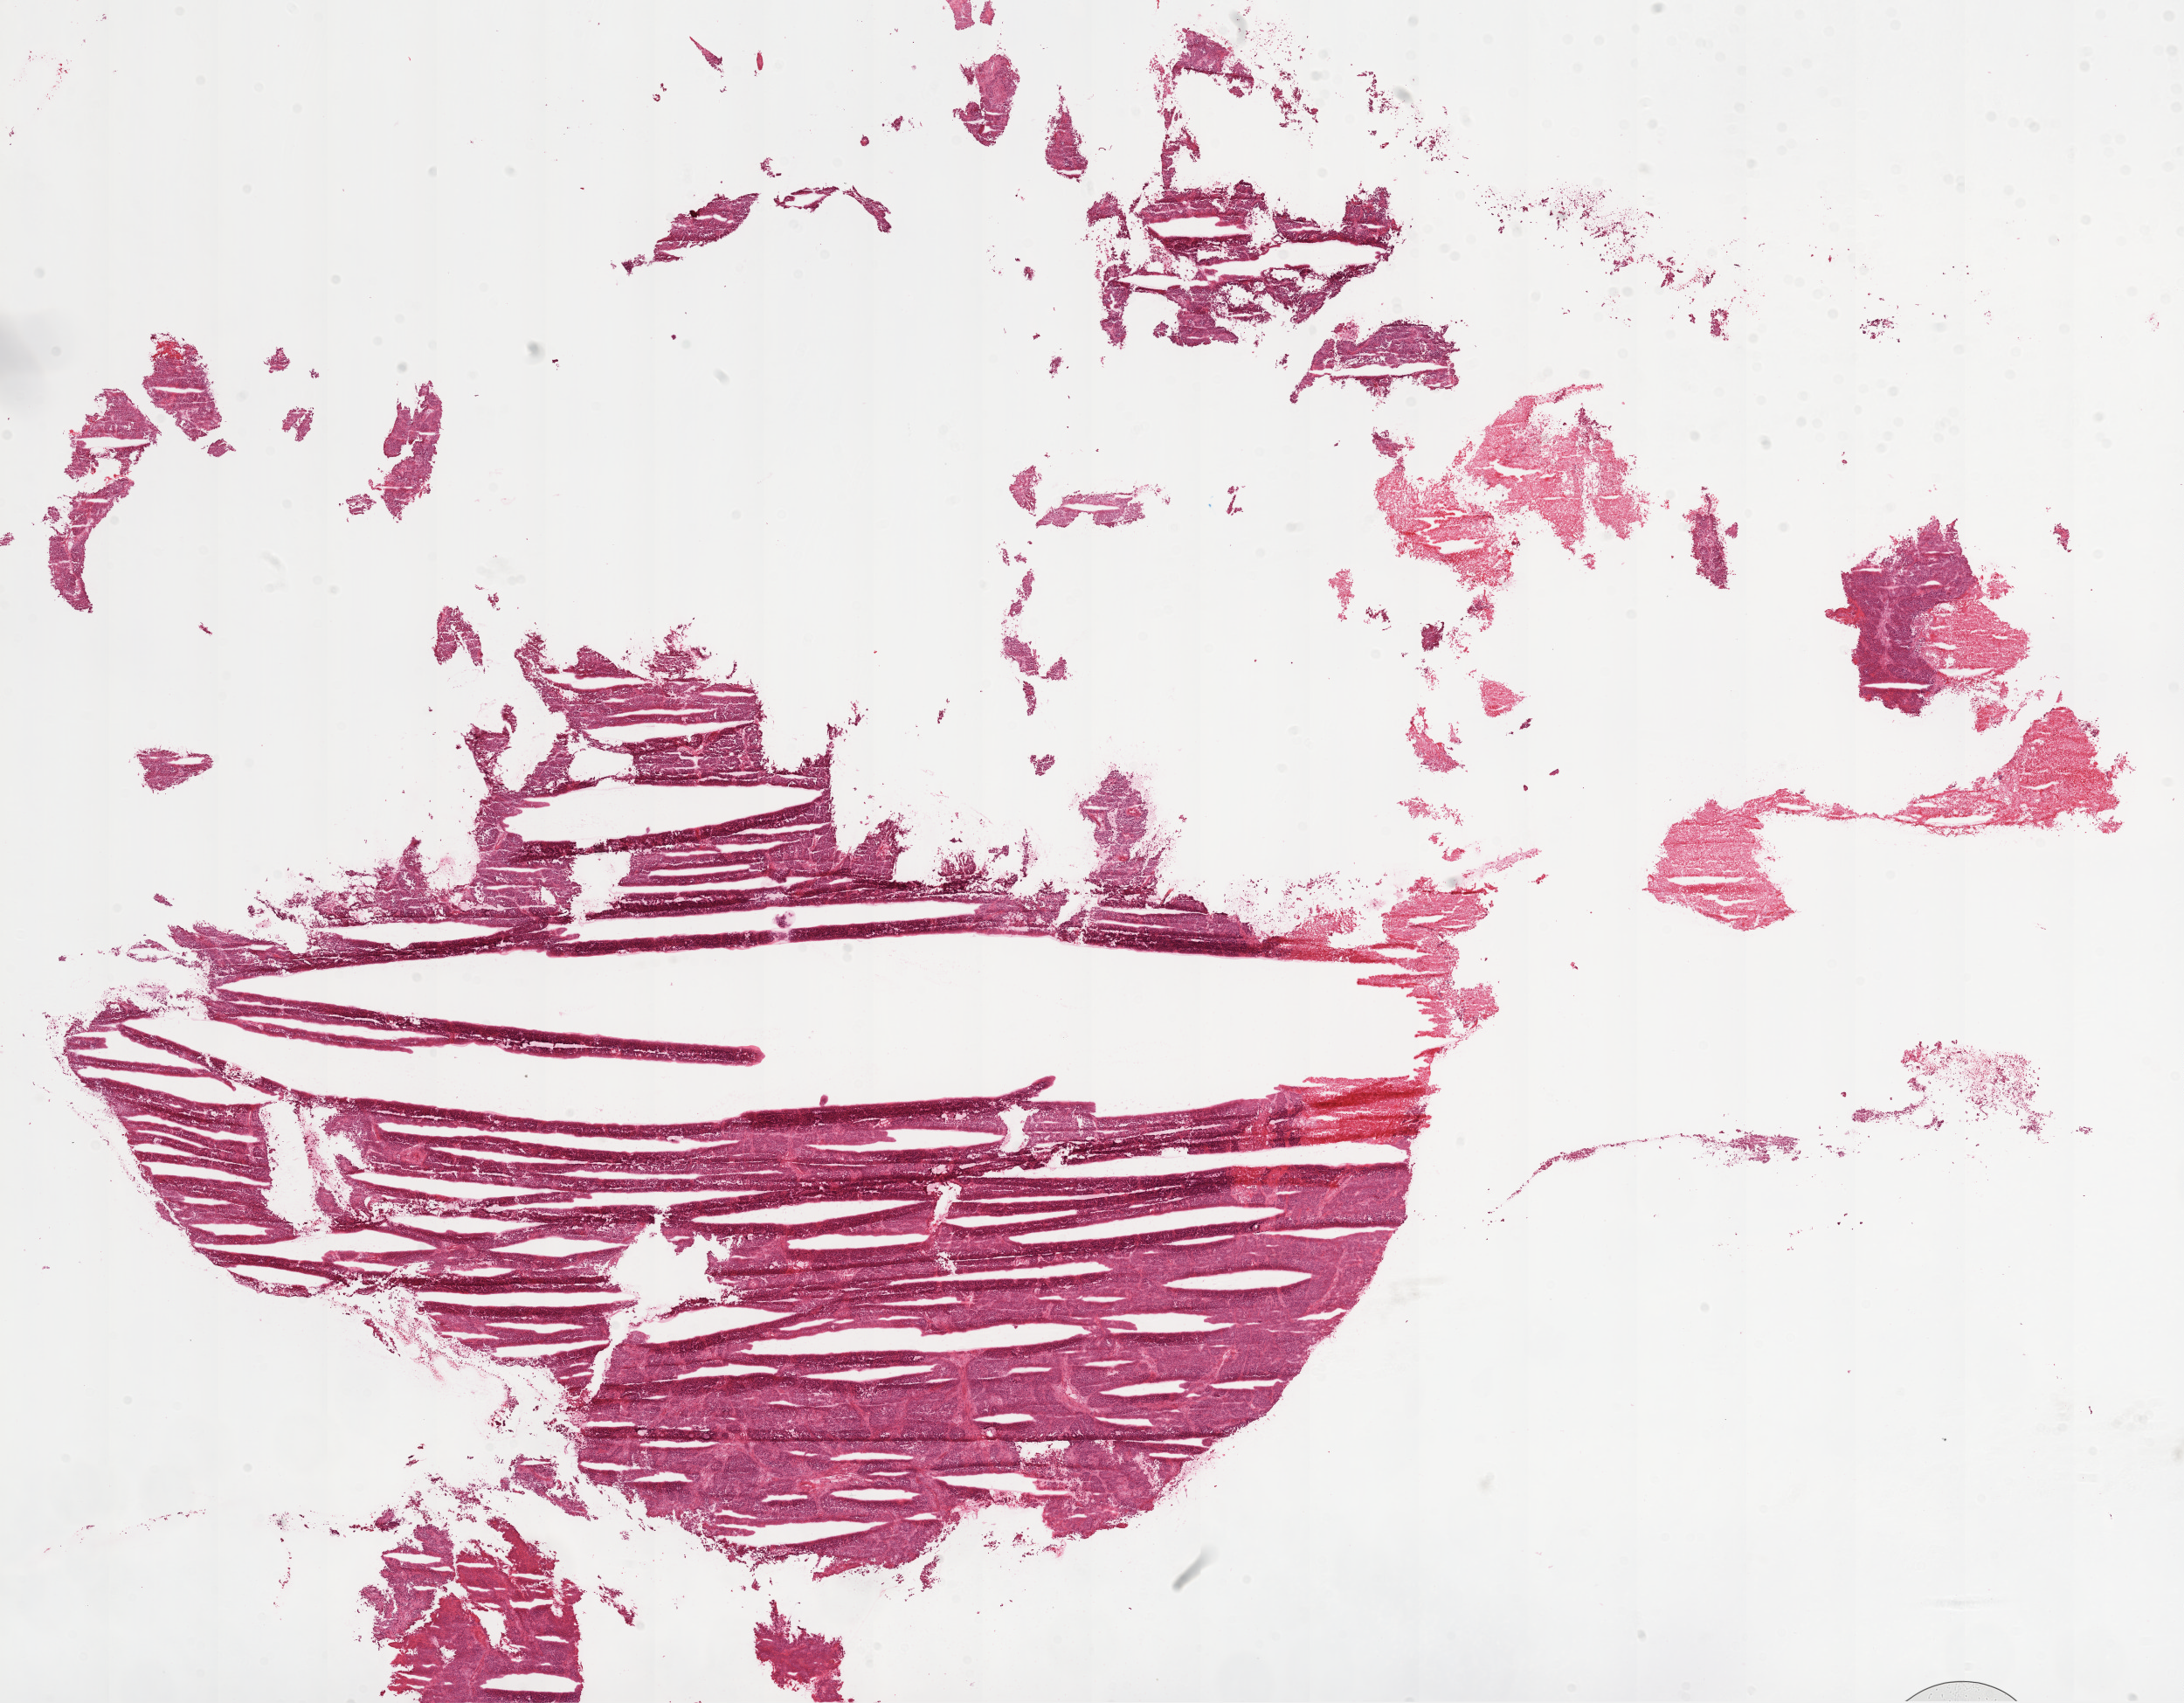
Whole-slide histology image, H&E-stained — low-resolution overview of the scanned area, about 20.1 x 15.6 mm (from a 20x scan). Frozen section from the top of the tissue portion. Recurrent tumour sample from the ovary. Female, age 40 years at initial diagnosis. Slide review estimates, as recorded: tumour cells 80%, tumour nuclei 85%, normal cells 0%, stromal cells 5%, necrosis 5%.
* this section: recurrent tumour
* patient diagnosis: Serous cystadenocarcinoma, NOS